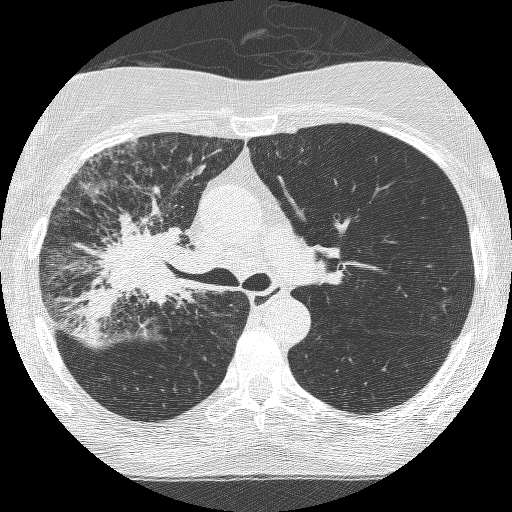
Axial slice from a low-dose chest CT screening exam. Third annual screen. Lung window (W 1500 / L -600 HU). 1.25 mm slice thickness. Female participant, aged 64 years at enrolment. Former smoker at enrolment.
- Expert reader's lesion annotation, bounding box [x1, y1, x2, y2] px = [84, 211, 204, 332].
- Reader record for this screening exam (exam-level; its link to the box is not recorded): non-calcified nodule or mass ≥4 mm, right upper lobe, 49 × 43 mm, spiculated (stellate) margins, soft tissue attenuation, pre-existing on the prior screen: yes; interval growth: yes.
- Later outcome: lung cancer diagnosed 7 days after this screen — adenocarcinoma, NOS, right upper lobe, right middle lobe, right hilum, stage IV (AJCC 6th edition), 85 mm at pathology.